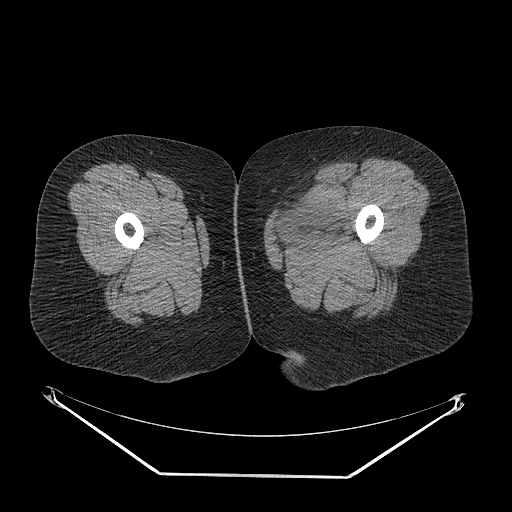
CT of an extremity soft-tissue mass (from a PET/CT study), one axial slice. Position 16 of 267 along the scan axis. Reconstruction kernel STANDARD. 140 kVp. Soft-tissue window (W 400 / L 40 HU). 3.75 mm slice thickness. 512 × 512 image matrix, field of view 500 × 500 mm. Female patient. Case-level facts recorded for this patient, not image findings: histological type: myxofibrosarcoma; grade: intermediate; site of the primary tumour: left thigh.
Outlined on this slice (expert contour drawn on MRI and transferred to this co-registered scan by the dataset authors):
- gross tumour volume including surrounding oedema: bounding box [x1, y1, x2, y2] px = [276, 198, 352, 247]
- gross tumour volume (mass): [286, 198, 341, 232]